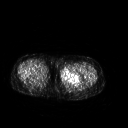
FDG PET of an extremity soft-tissue mass (from a PET/CT study), one axial slice. Slice 229 of 267 in the series (ordered by position). 3.27 mm slice thickness. 128 × 128 image matrix, field of view 500 × 500 mm. Female patient, age 42 years. Case-level facts recorded for this patient, not image findings: histological type: pleiomorphic leiomyosarcoma; grade: intermediate; site of the primary tumour: left thigh.
Annotated regions visible in this slice (expert contour drawn on MRI and transferred to this co-registered scan by the dataset authors):
- gross tumour volume including surrounding oedema: bounding box [x1, y1, x2, y2] px = [60, 67, 83, 82]
- gross tumour volume (mass): [61, 67, 80, 82]